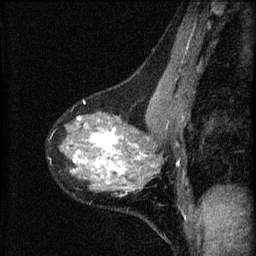
Breast MRI (dynamic contrast-enhanced), one sagittal slice; position 36 of 60 along the scan axis; dynamic contrast-enhanced series, image 2 of 4 at this slice position (ordered by acquisition); 1.5 T; TE 4.2 ms, TR 8.2 ms; 256 × 256 image matrix, field of view 180 × 180 mm. Patient: female, 41 years.
Structures marked on this image (semi-automatically segmented with operator editing):
- analysis volume of interest (the breast-tissue region the enhancement analysis was run in; not a lesion): bounding box [x1, y1, x2, y2] px = [61, 91, 166, 197]
- tumour enhancement mask (voxels above the 70 % enhancement threshold inside the analysis volume of interest): [72, 127, 147, 196]